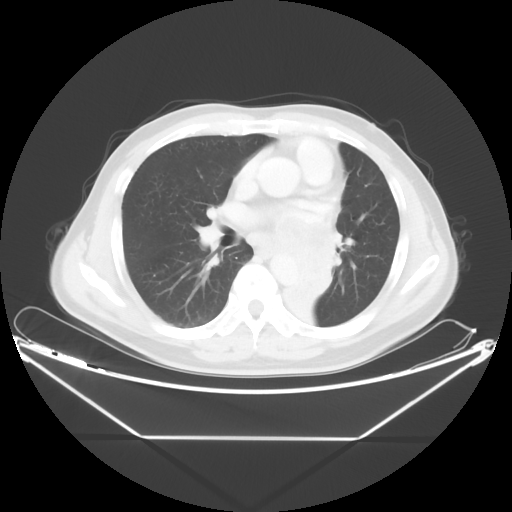
Chest CT, one axial slice. Position 24 of 48 along the scan axis. 120 kVp. Lung window (W 1500 / L -600 HU). 5 mm slice thickness. 512 × 512 image matrix, field of view 438 × 438 mm. Patient: male, 58 years. Case-level facts recorded for this patient, not image findings: clinical TNM (as recorded): T3 N3 M0.
Annotated regions visible in this slice (rectangle marked by the reading radiologist):
- lung tumour (recorded histology: squamous cell carcinoma): bounding box [x1, y1, x2, y2] px = [282, 209, 346, 334]